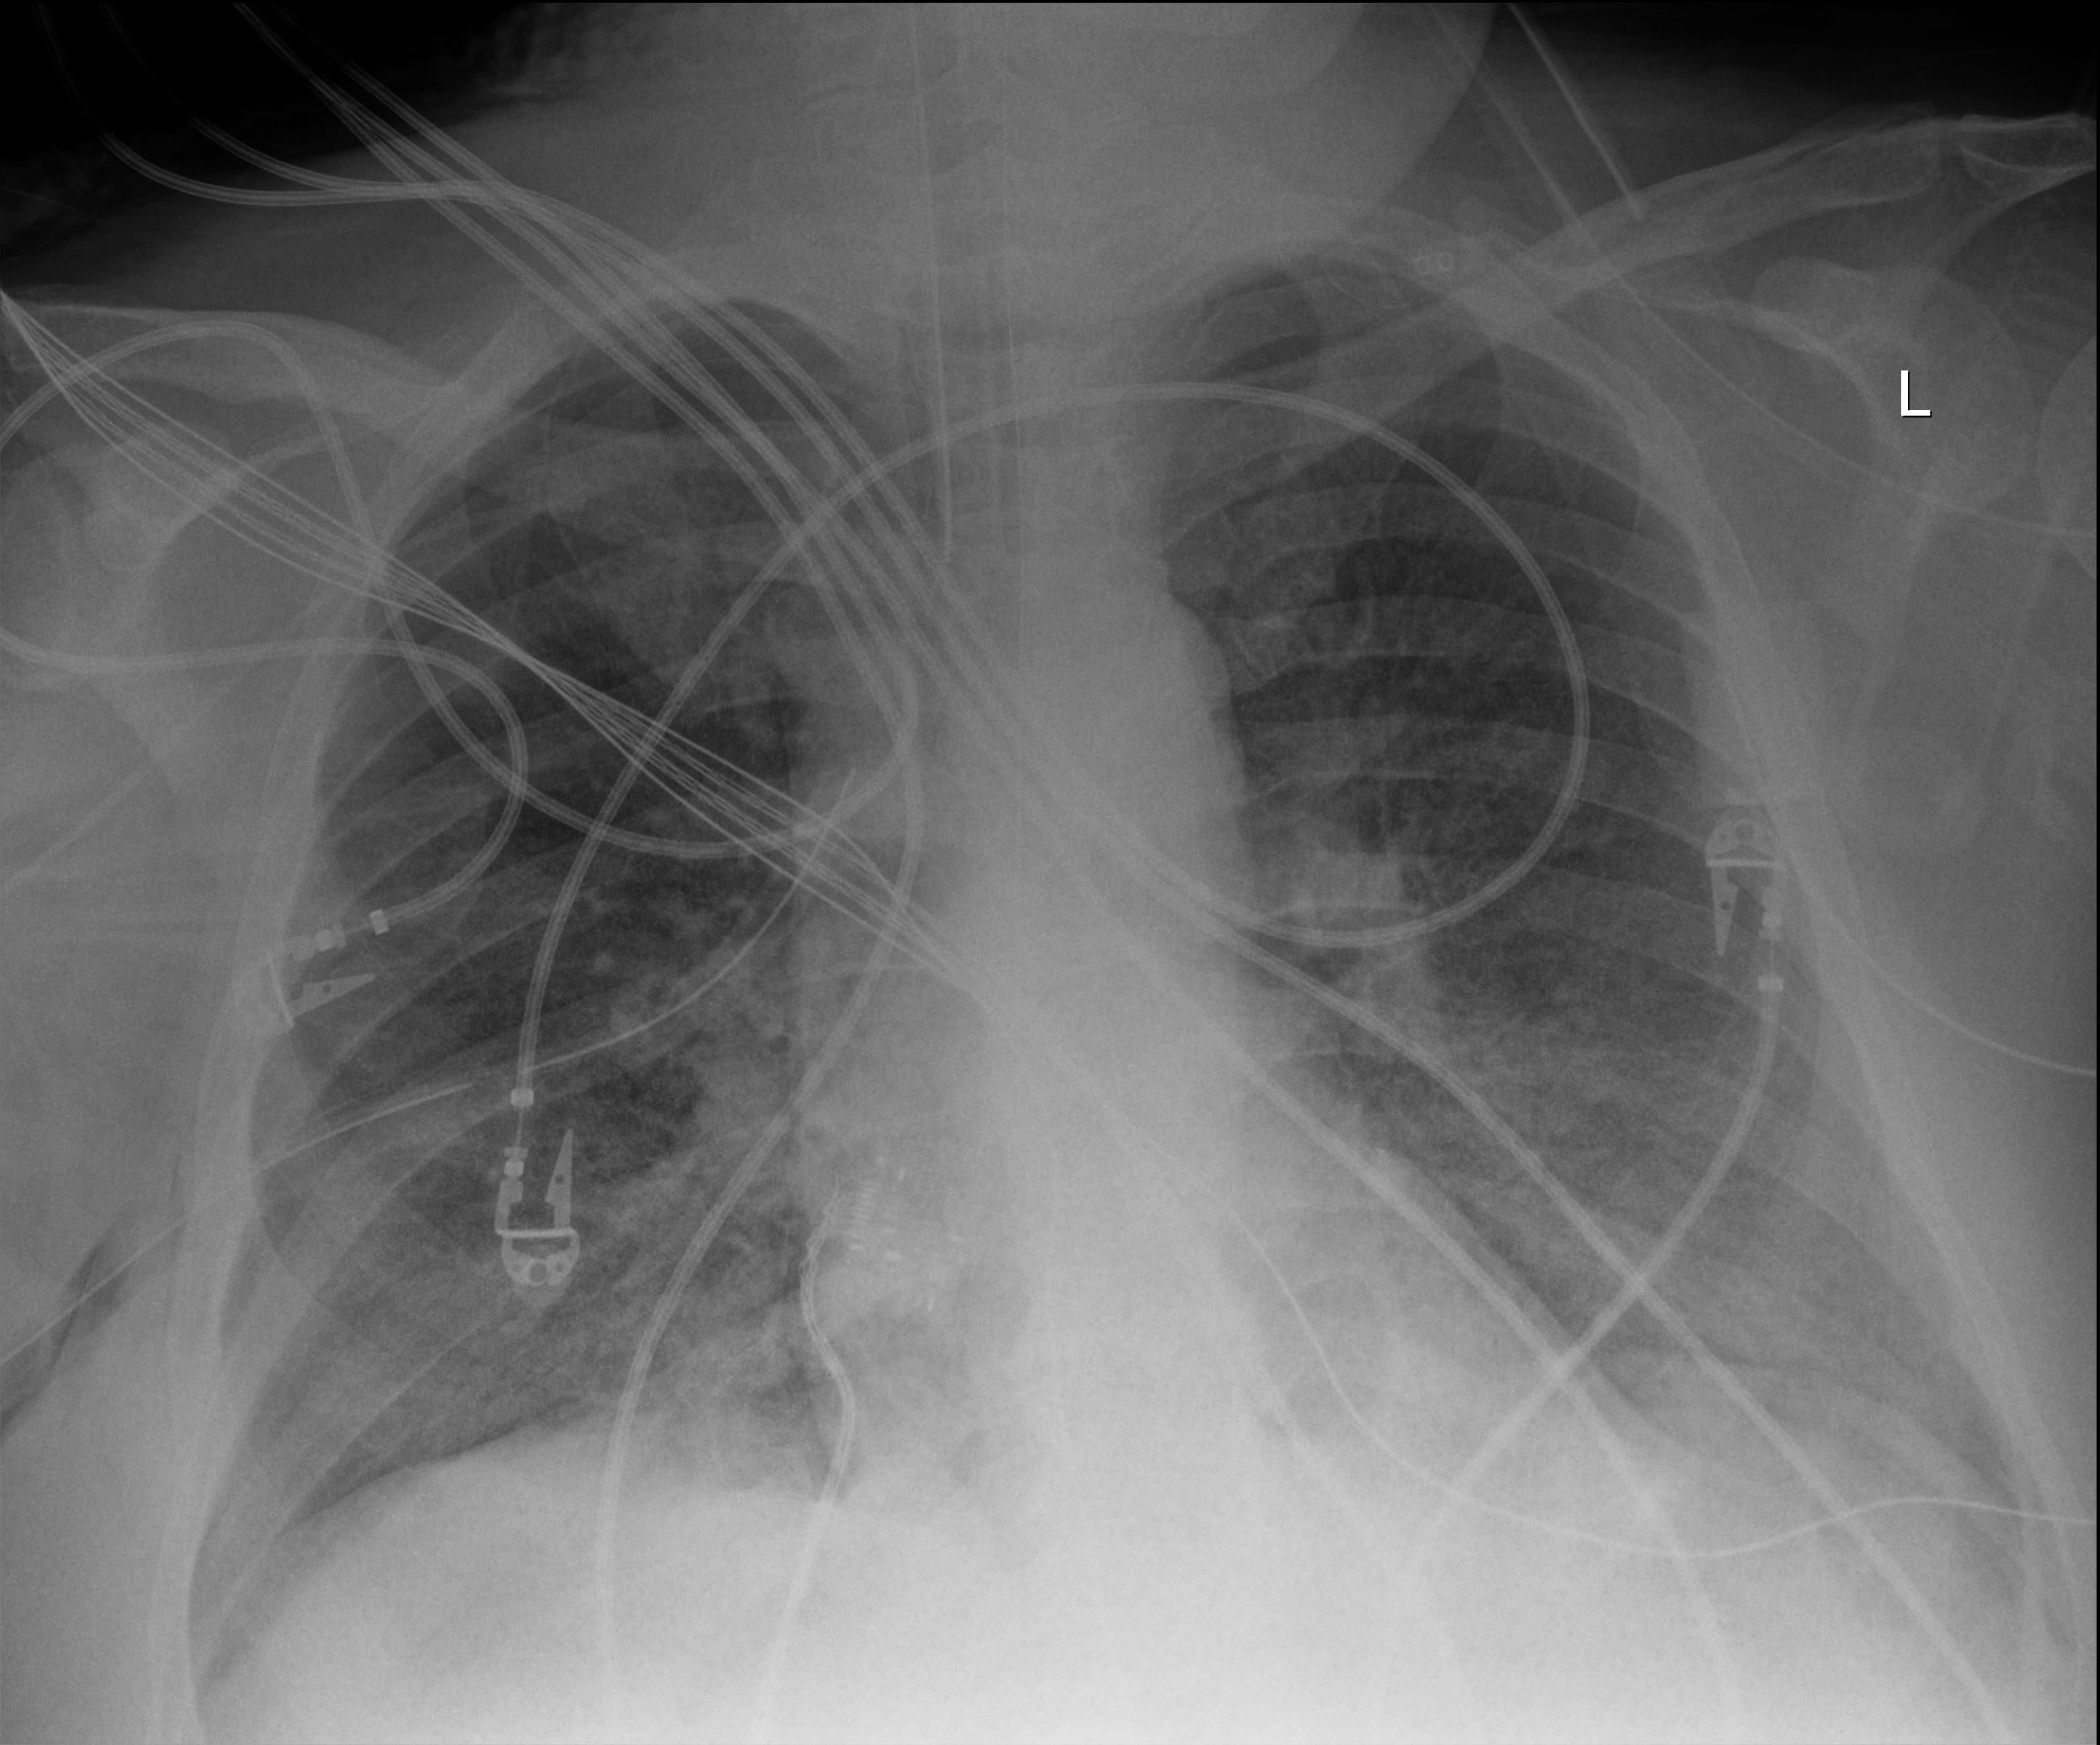
Chest X-ray (portable), anteroposterior (AP) projection. Patient hospitalised with COVID-19, aged 18–59 years.
Hospital-stay facts (about this admission, not read from this image; timing relative to this image not recorded):
- admitted to intensive care during this hospital stay: yes
- chronic kidney disease (admission record): no